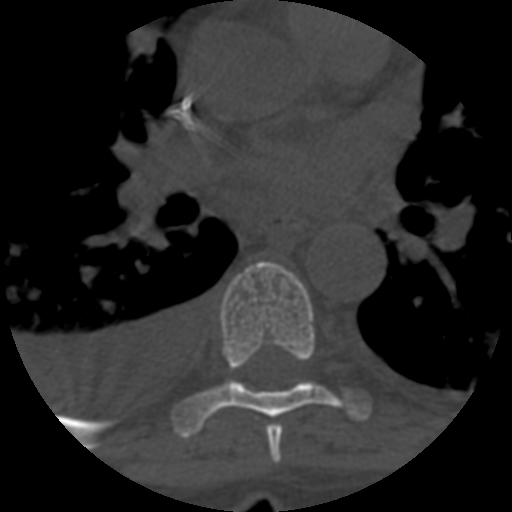
CT including the spine, one axial slice. Position 417 of 708 along the scan axis. One of 3 acquisitions stored at this slice position. Bone window (W 1800 / L 400 HU). 1.25 mm slice thickness. 512 × 512 image matrix. Patient age 55 years. Case-level facts recorded for this patient, not image findings: primary cancer: colon; vertebrae with lytic lesions (as recorded): T12, L1, L5.
Annotated regions visible in this slice (semi-automatically segmented with operator editing):
- T6 vertebra: bounding box (x1, y1, x2, y2) in pixels: (266, 424, 283, 463)
- T7 vertebra: (173, 261, 369, 437)